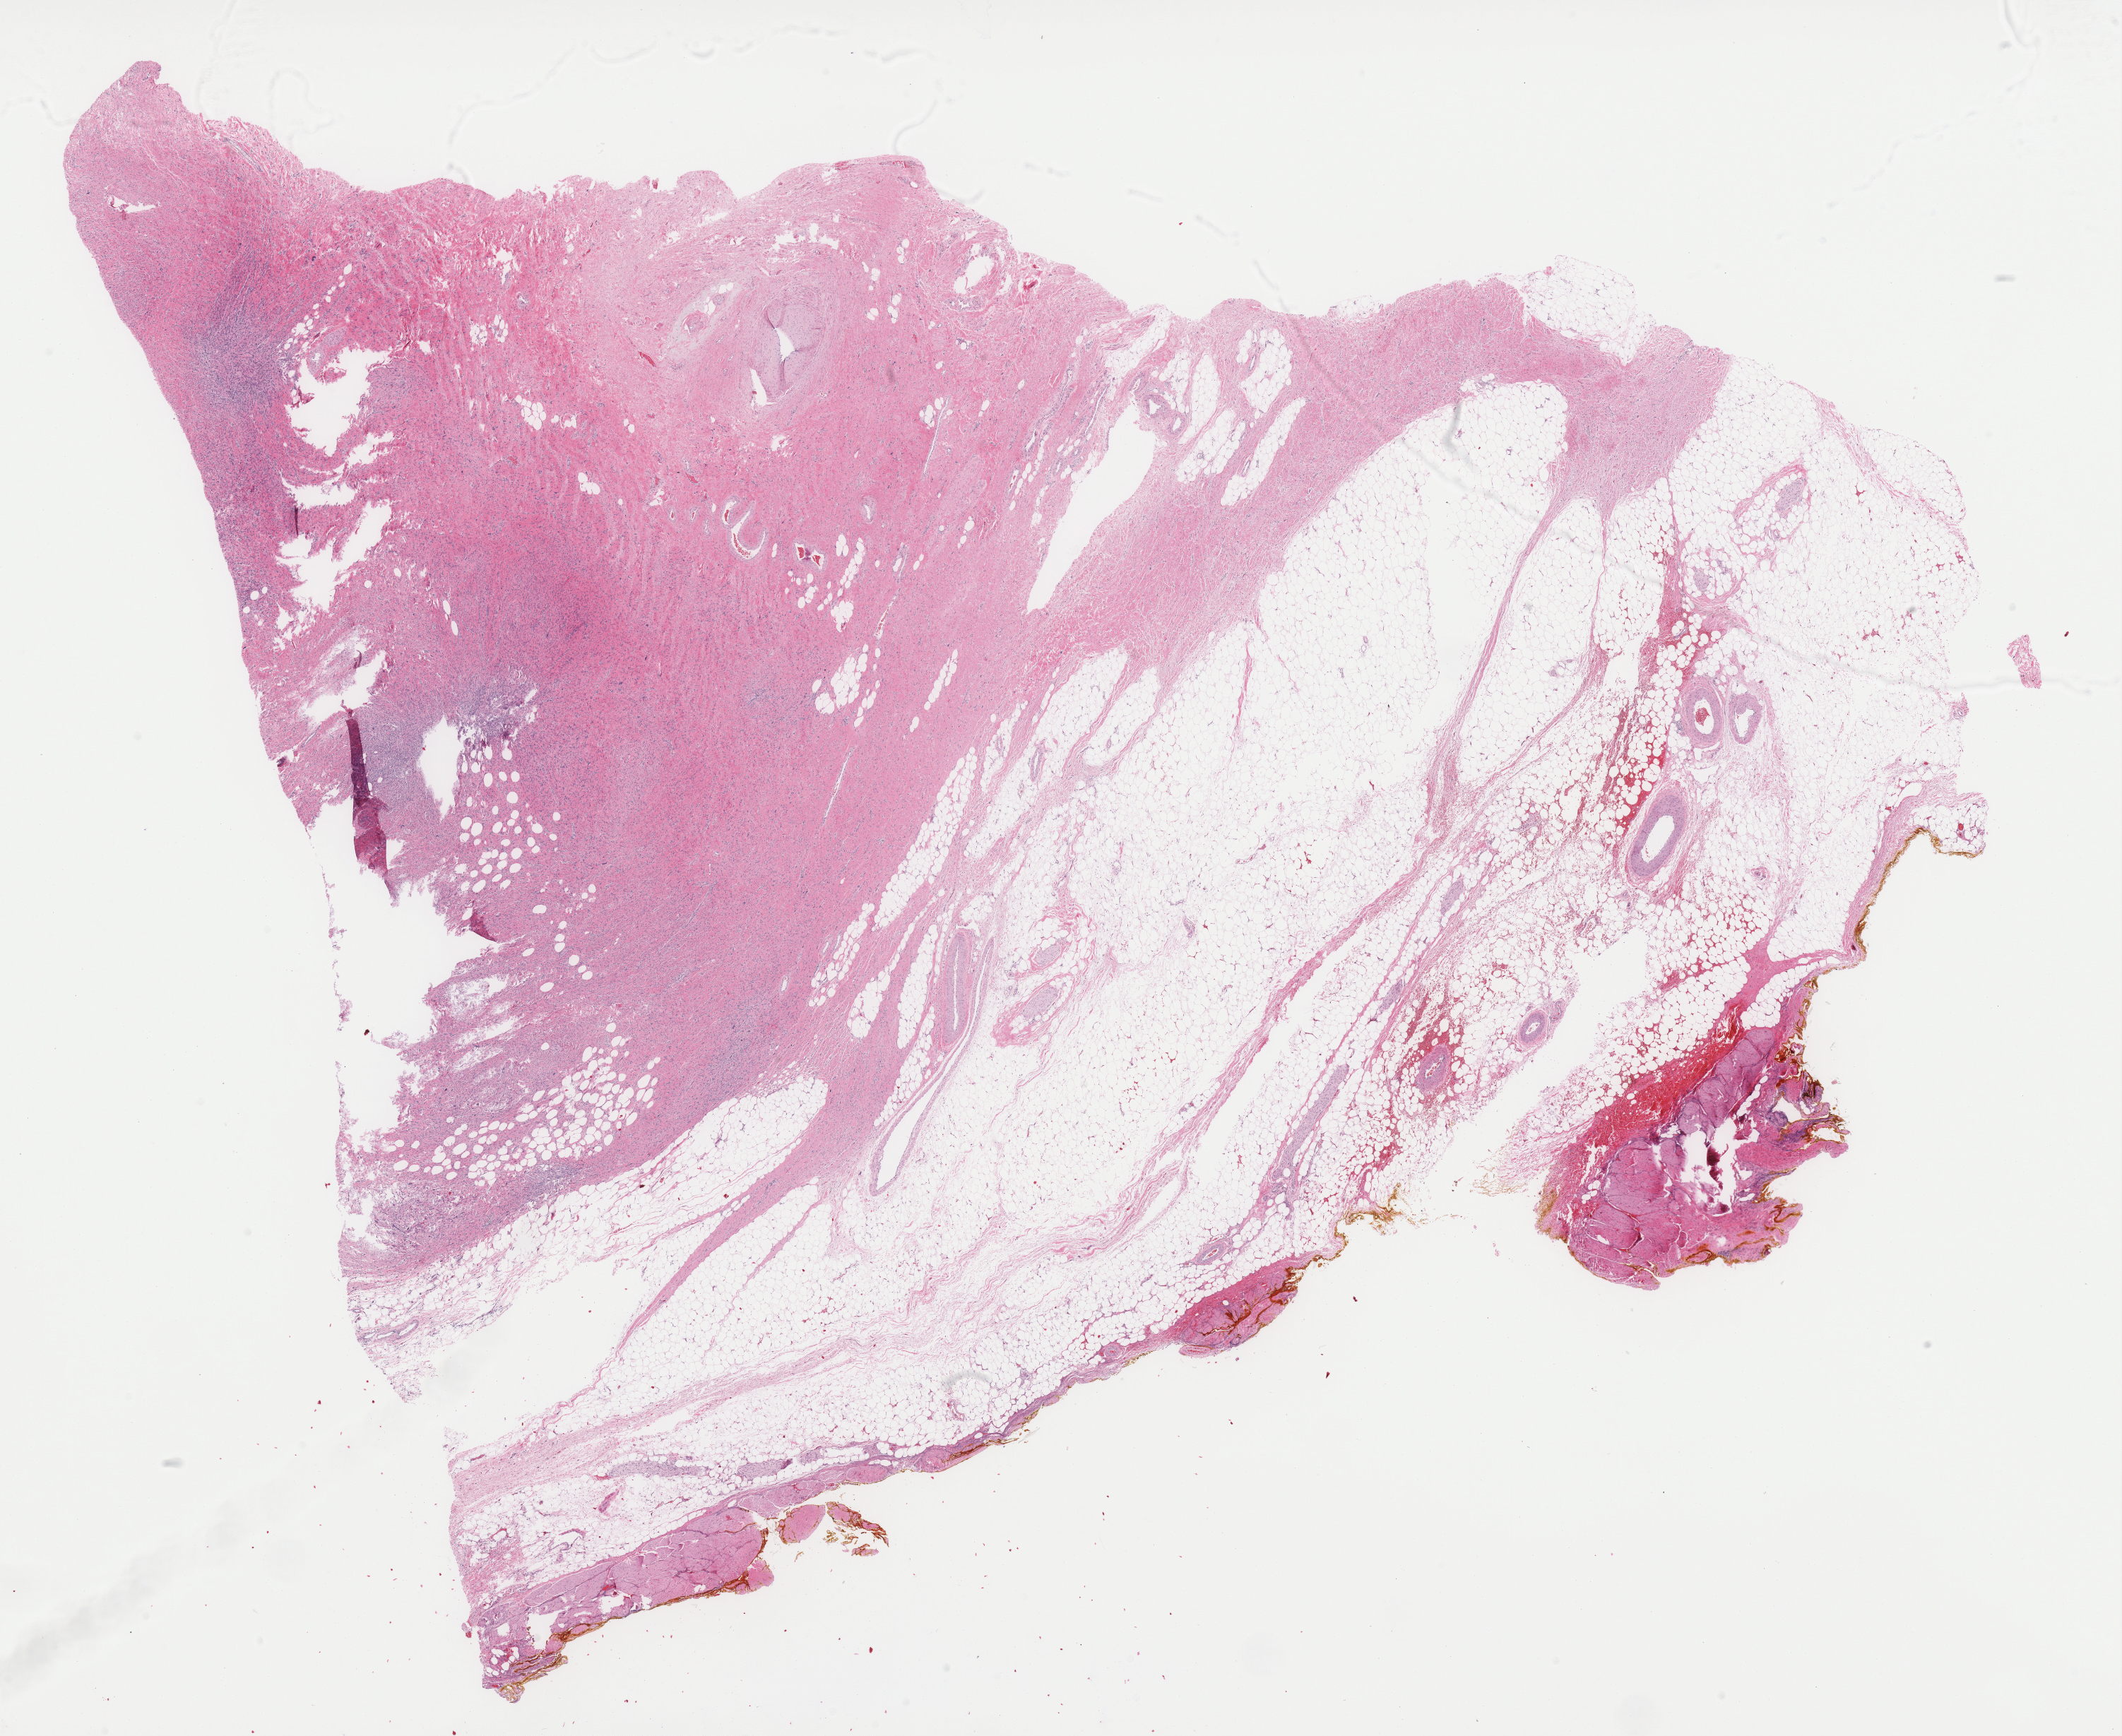
H&E whole-slide image, low-resolution overview of the scanned area, about 24.0 x 19.6 mm. Formalin-fixed paraffin-embedded (FFPE) diagnostic section. Sample: primary tumour, retroperitoneum and peritoneum. Male patient; age at initial diagnosis 34 years.
Diagnosis: Dedifferentiated liposarcoma.